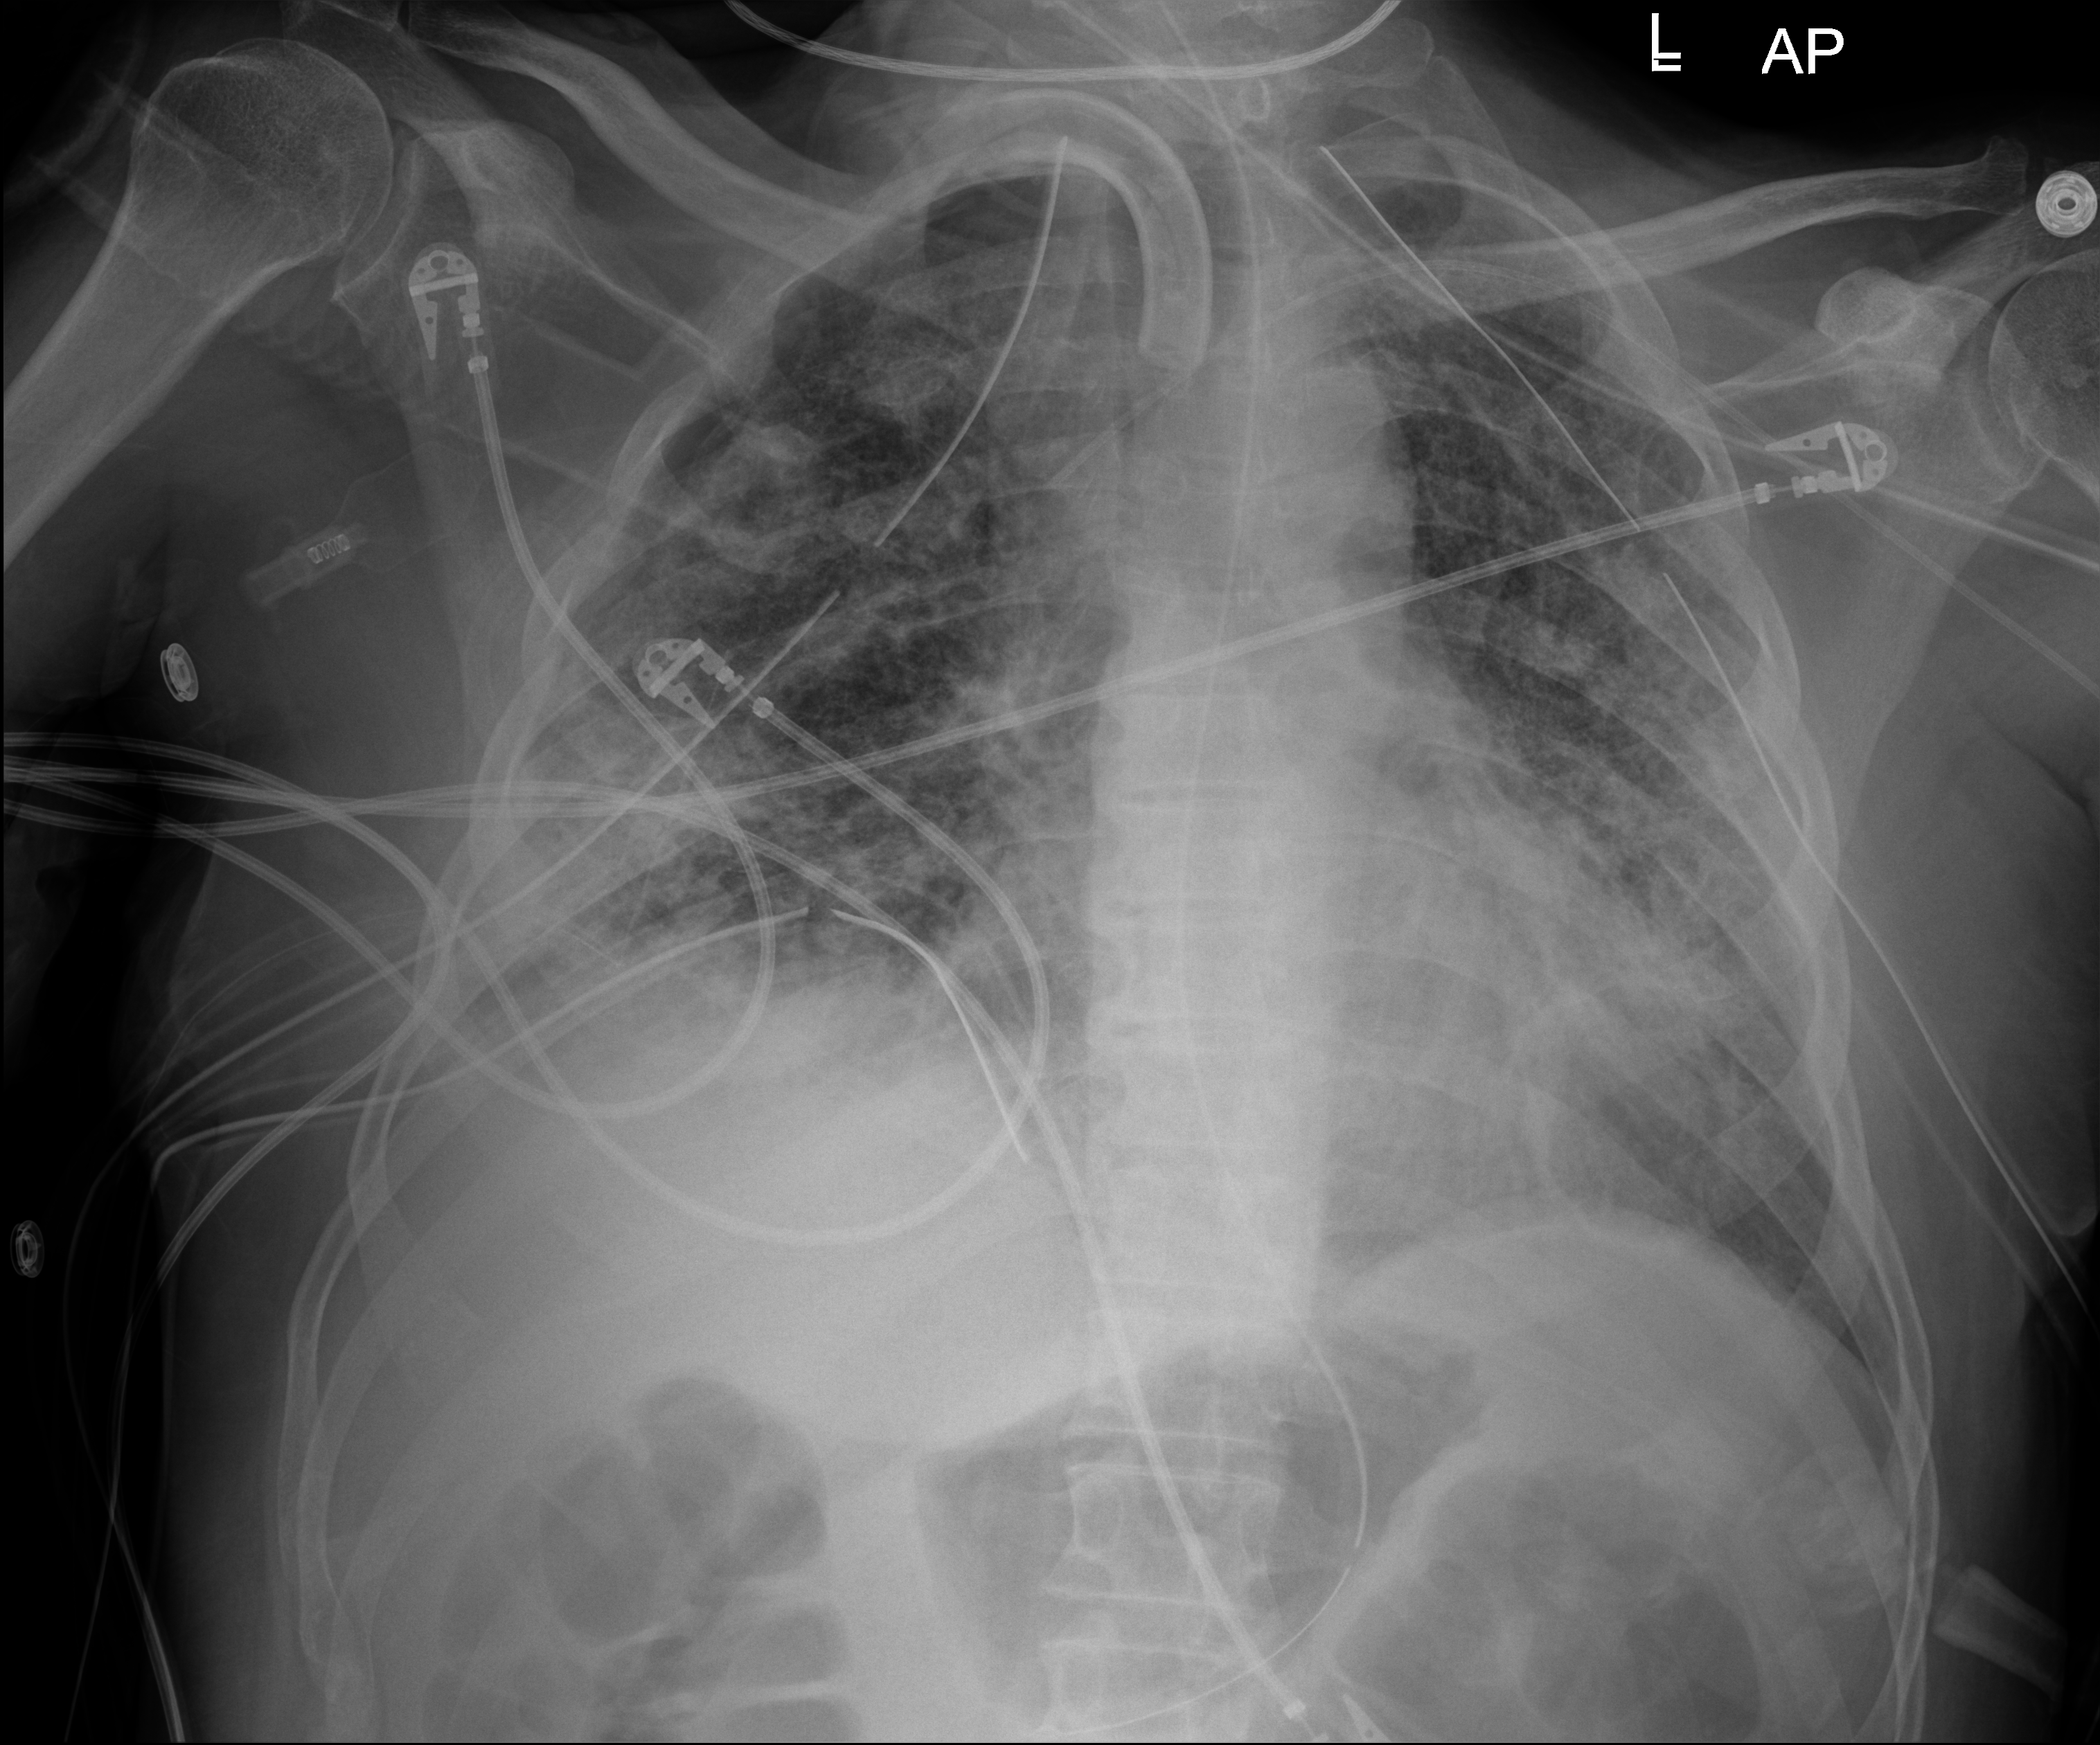
Chest X-ray (portable); anteroposterior (AP) projection. Male patient hospitalised with COVID-19, age 18–59 years.
Admission-level facts for this patient (not findings on this image; timing relative to this image not recorded): other chronic lung disease (admission record): no; chronic kidney disease (admission record): no.